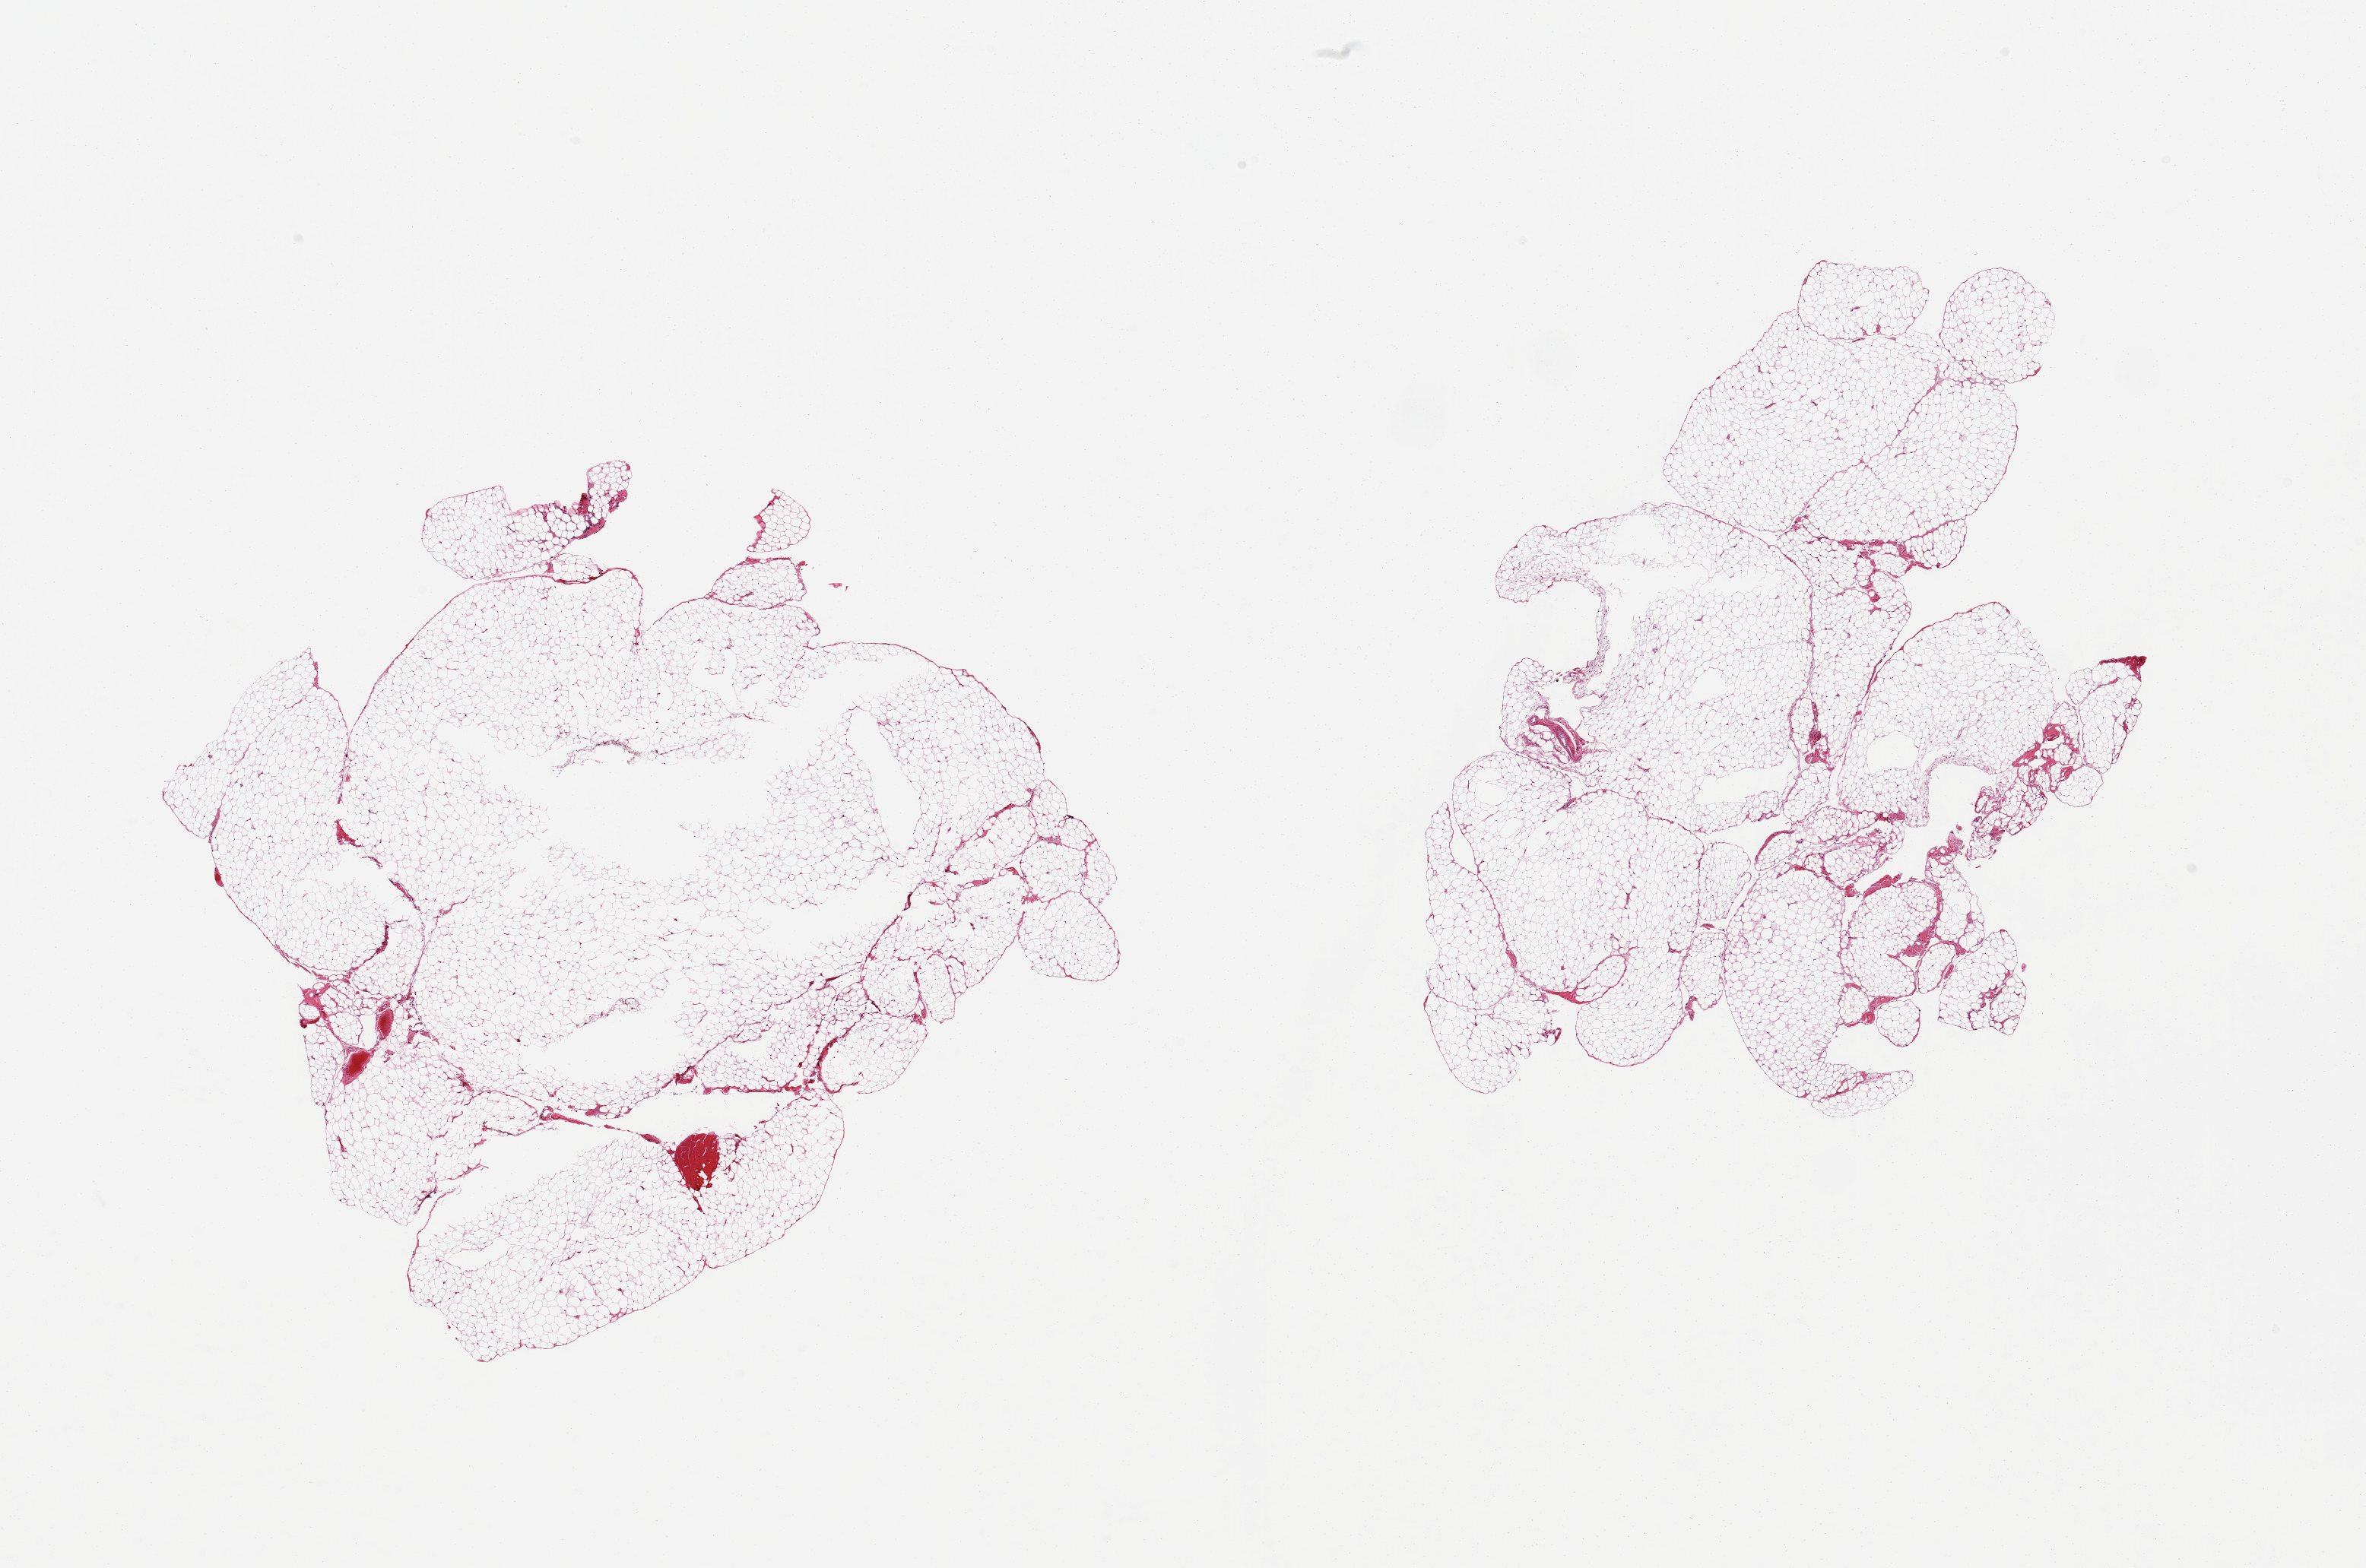
Digitized H&E-stained section — whole scanned area (about 24.6 x 16.3 mm, slide scanned at 20x) shown as a low-resolution overview, PAXgene-fixed, paraffin-embedded tissue, section of omentum (target tissue), donor tissue sample. Donor: male.
Pathologist's review note for this sample: 2 pieces; lobulated mature adipose tissue, 1 piece has central defect (?poor fixation), fragment of skeletal muscle.